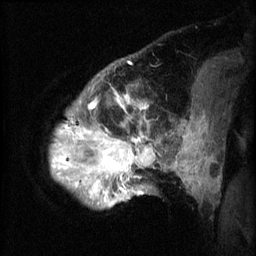
Breast MRI (dynamic contrast-enhanced), one sagittal slice. Position 12 of 60 along the scan axis. 3 images stored at this slice position (order not interpretable as contrast timing). 1.5 T. TE 4.2 ms, TR 8.2 ms. 256 × 256 image matrix. Patient: female, 50 years.
Annotated regions visible in this slice (semi-automatic segmentation, software-assisted and operator-edited):
- analysis volume of interest (the breast-tissue region the enhancement analysis was run in; not a lesion): bounding box (x1, y1, x2, y2) in pixels: (52, 64, 169, 209)
- tumour enhancement mask (voxels above the 70 % enhancement threshold inside the analysis volume of interest): (52, 90, 157, 205)